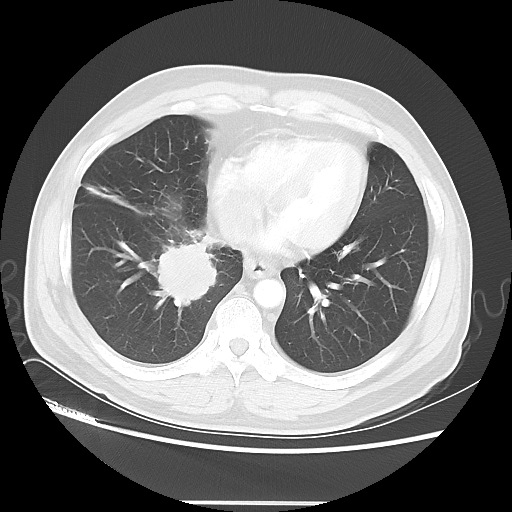
Chest CT, one axial slice. Position 15 of 48 along the scan axis. Reconstruction kernel LUNG. Lung window (W 1500 / L -600 HU). 5 mm slice thickness. 512 × 512 image matrix, field of view 390 × 390 mm. Male patient, age 53 years. Case-level facts recorded for this patient, not image findings: clinical TNM (as recorded): T2 N3 M0; histopathological grade: G3.
Annotated regions visible in this slice (rectangle marked by the reading radiologist):
- lung tumour (recorded histology: small cell carcinoma): box from (x=144, y=227) to (x=222, y=314) px